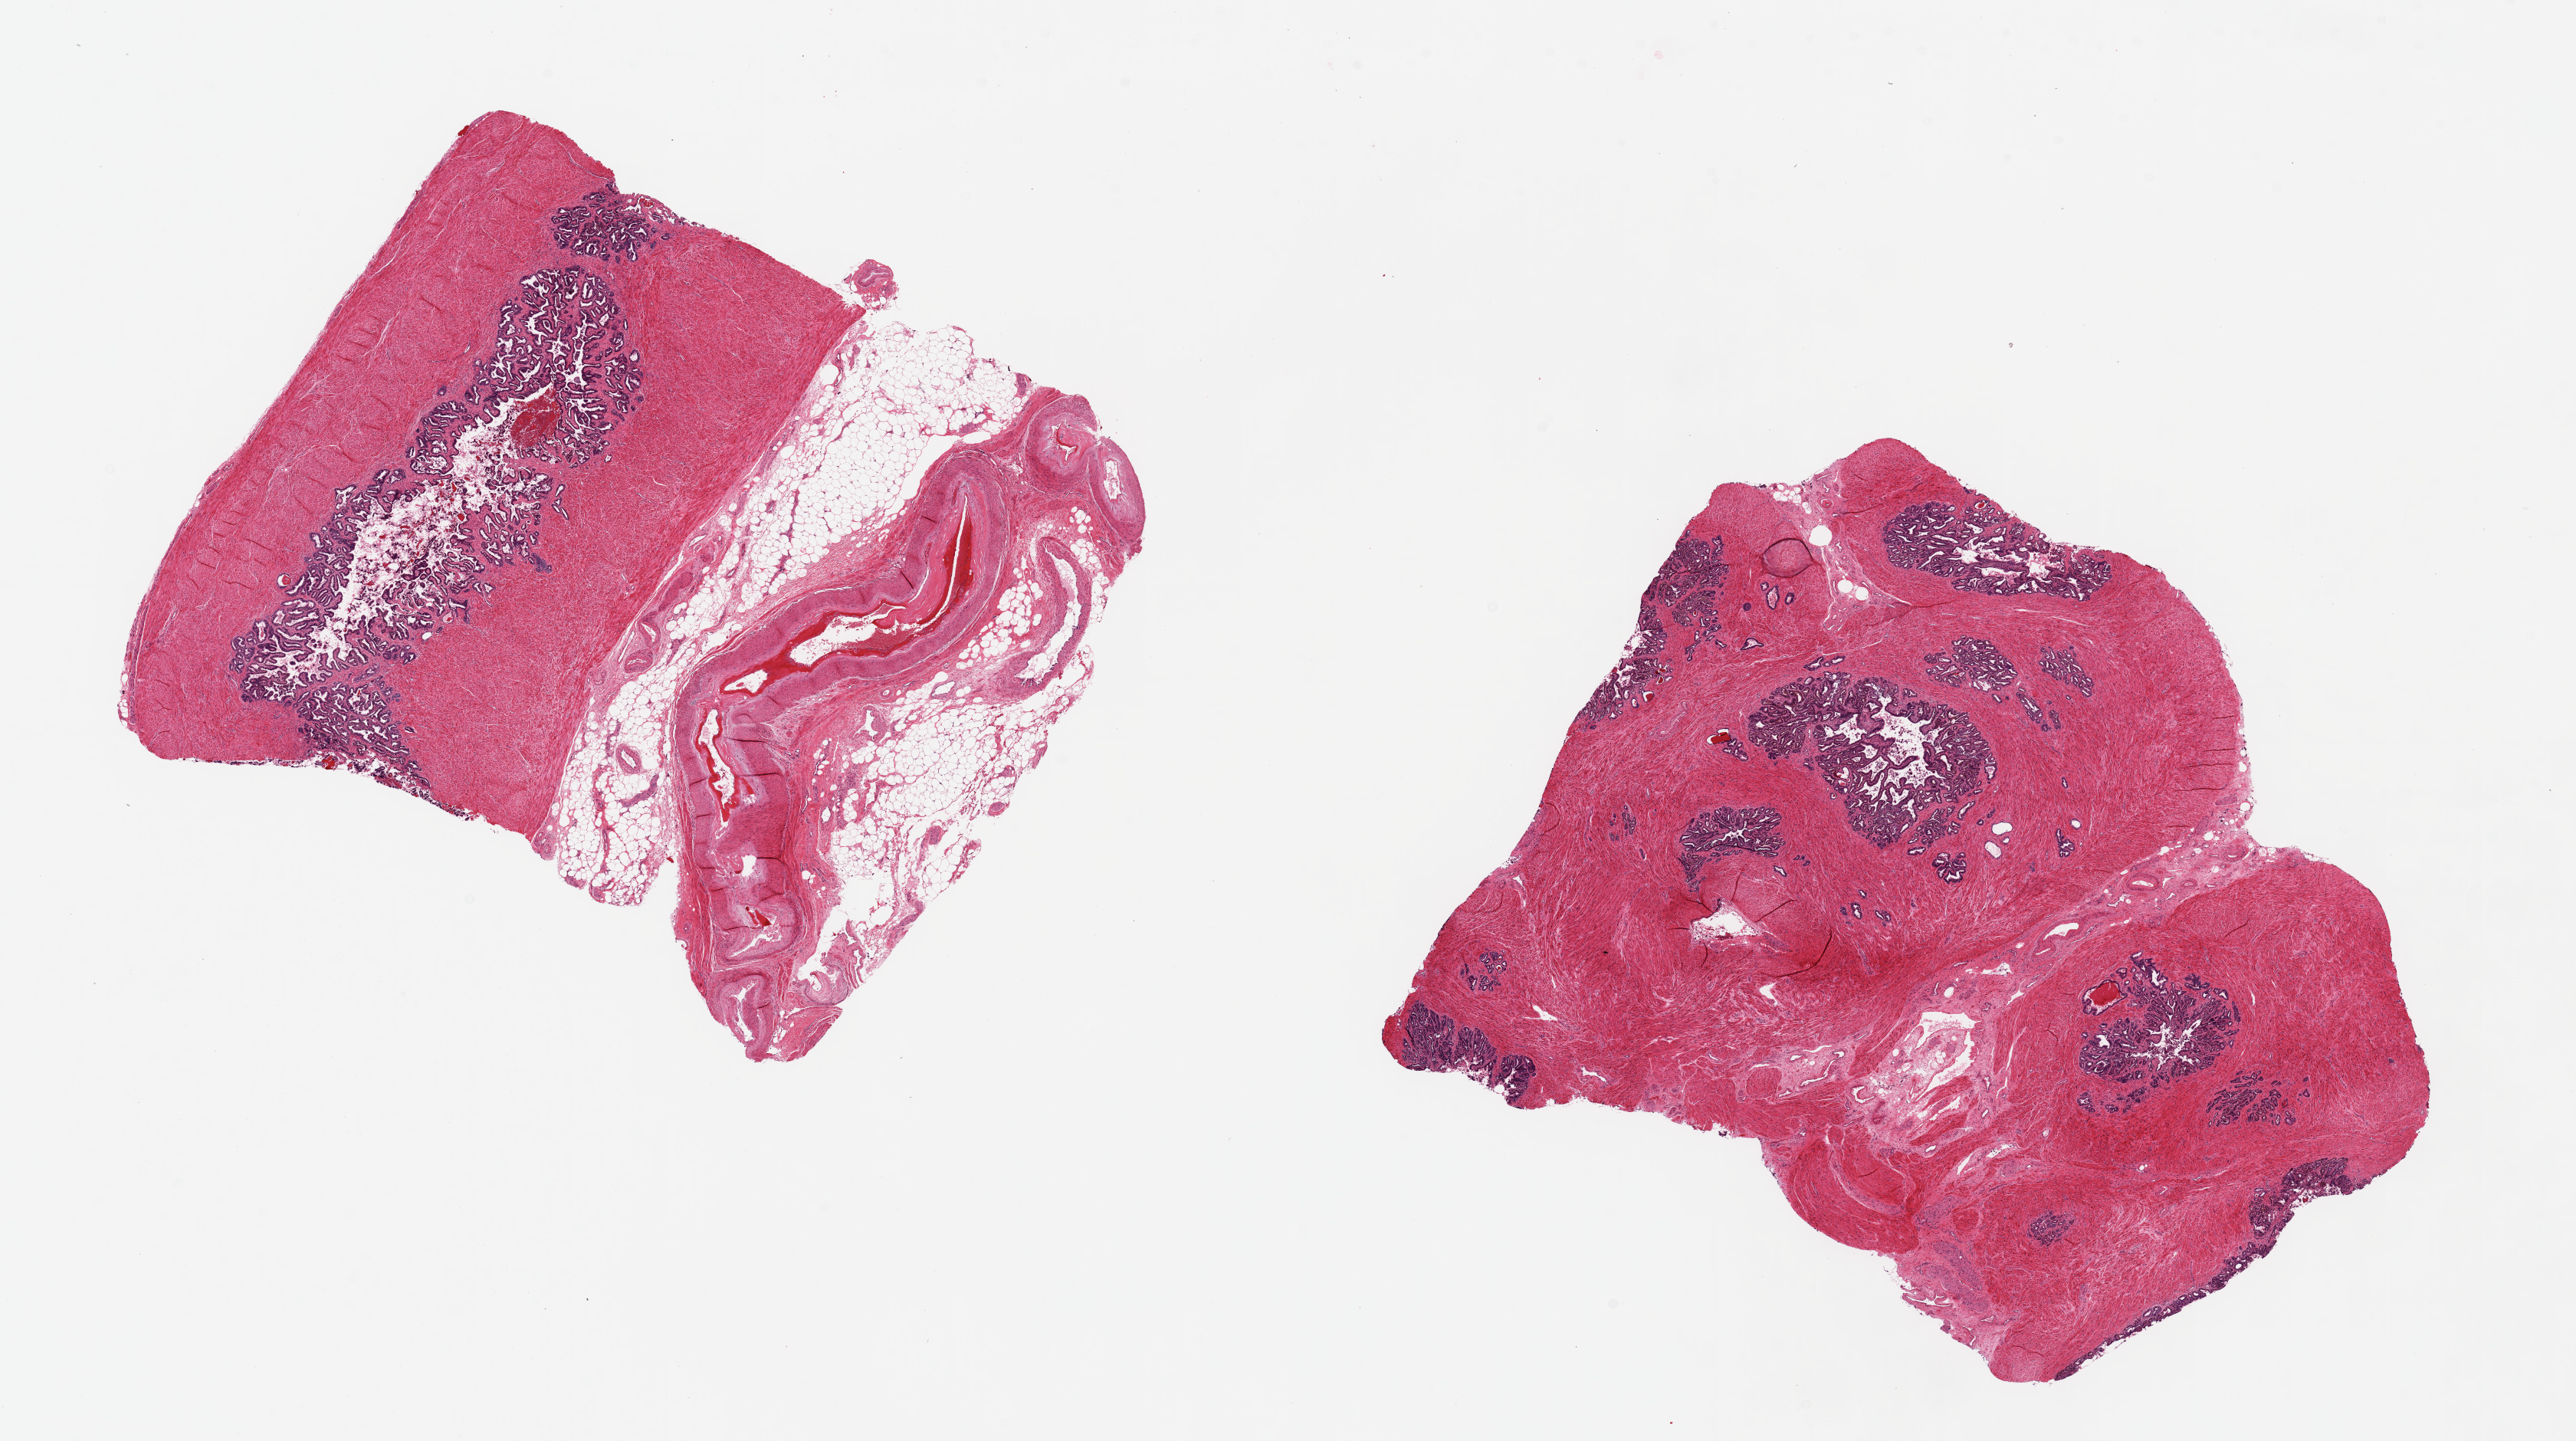
Whole-slide image, H&E stain, whole scanned area (about 26.6 x 14.9 mm) shown as a low-resolution overview. Male donor.
Specimen: PAXgene-fixed, paraffin-embedded tissue; sampled site (target tissue): prostate; tissue donor sample.